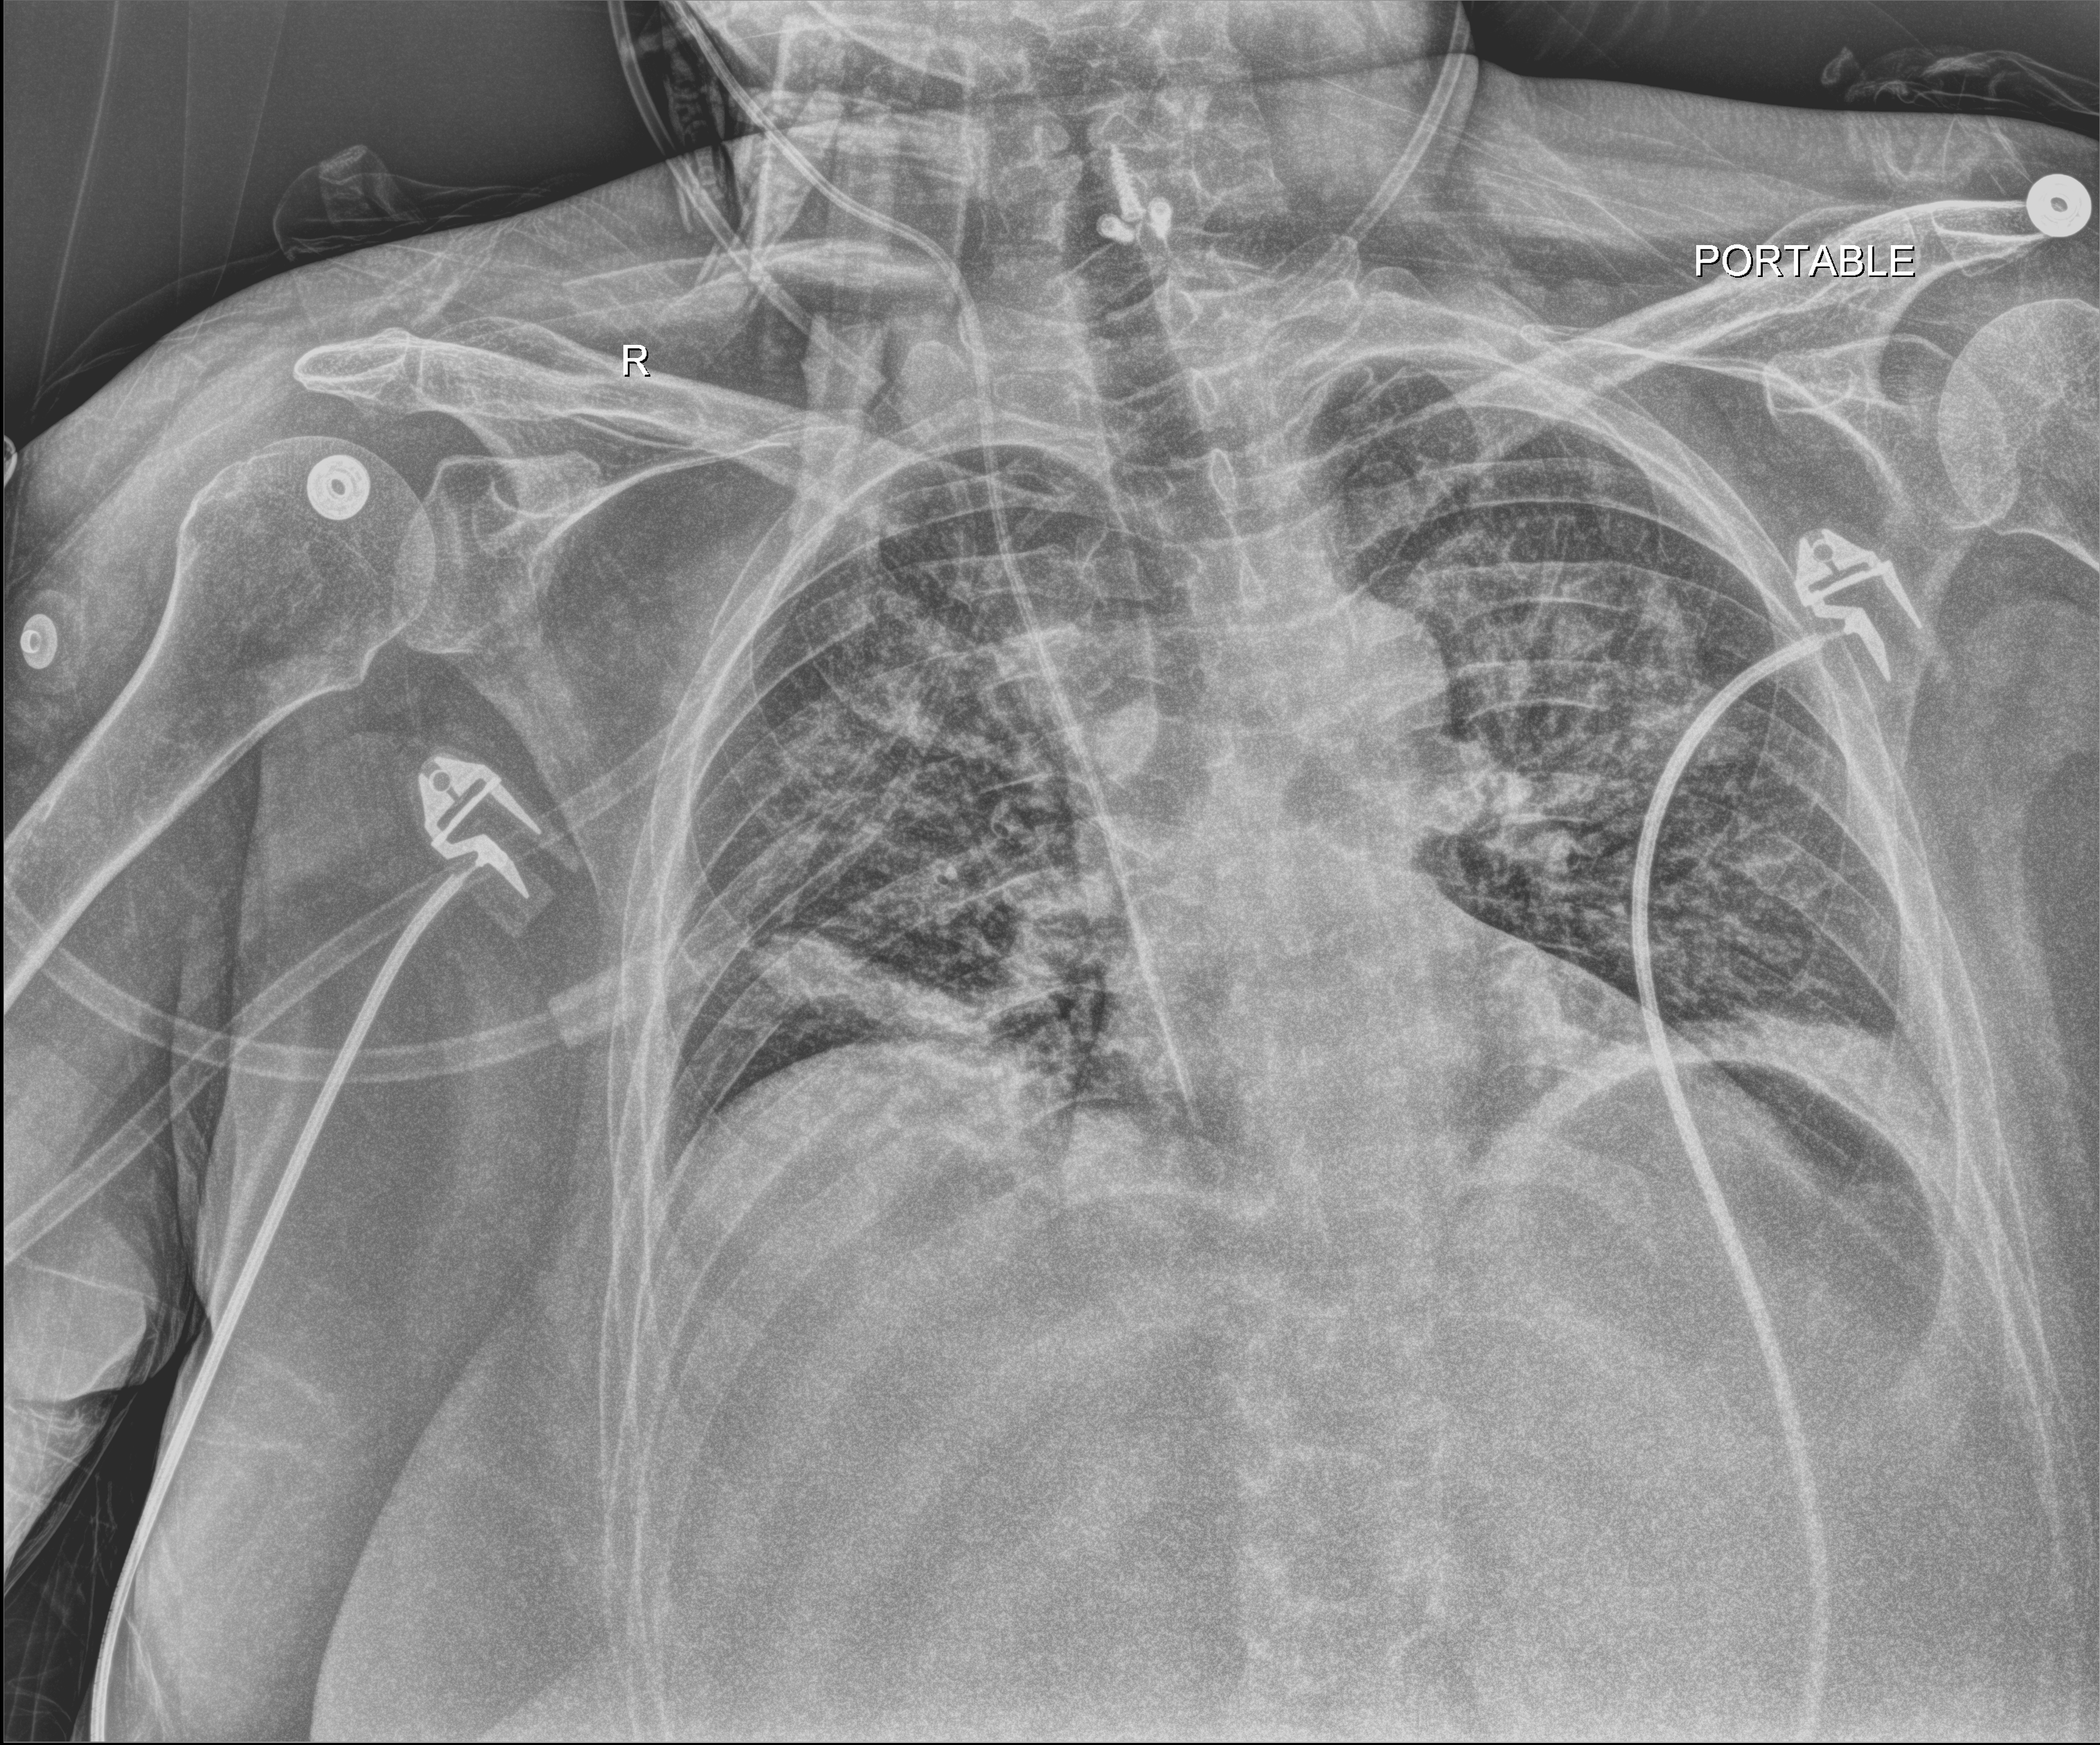
Chest X-ray (portable), anteroposterior (AP) projection. Female patient hospitalised with COVID-19, age 18–59 years.
From the hospital-stay record, not from the radiograph (when in the stay this image was taken is not recorded):
- mechanically ventilated during this hospital stay: no